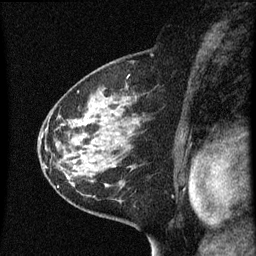
Breast MRI (dynamic contrast-enhanced), one sagittal slice; slice 36 of 60 in the series (ordered by position); dynamic contrast-enhanced series, image 2 of 3 at this slice position (ordered by acquisition); 1.5 T; TE 4.2 ms, TR 8 ms; 2 mm slice thickness; 256 × 256 image matrix, field of view 180 × 180 mm. Female patient, age 60 years.
Structures marked on this image (semi-automatic segmentation, software-assisted and operator-edited):
- analysis volume of interest (the breast-tissue region the enhancement analysis was run in; not a lesion): bounding box <48,82,143,183> (left, top, right, bottom; pixels)
- tumour enhancement mask (voxels above the 70 % enhancement threshold inside the analysis volume of interest): <75,122,134,169>